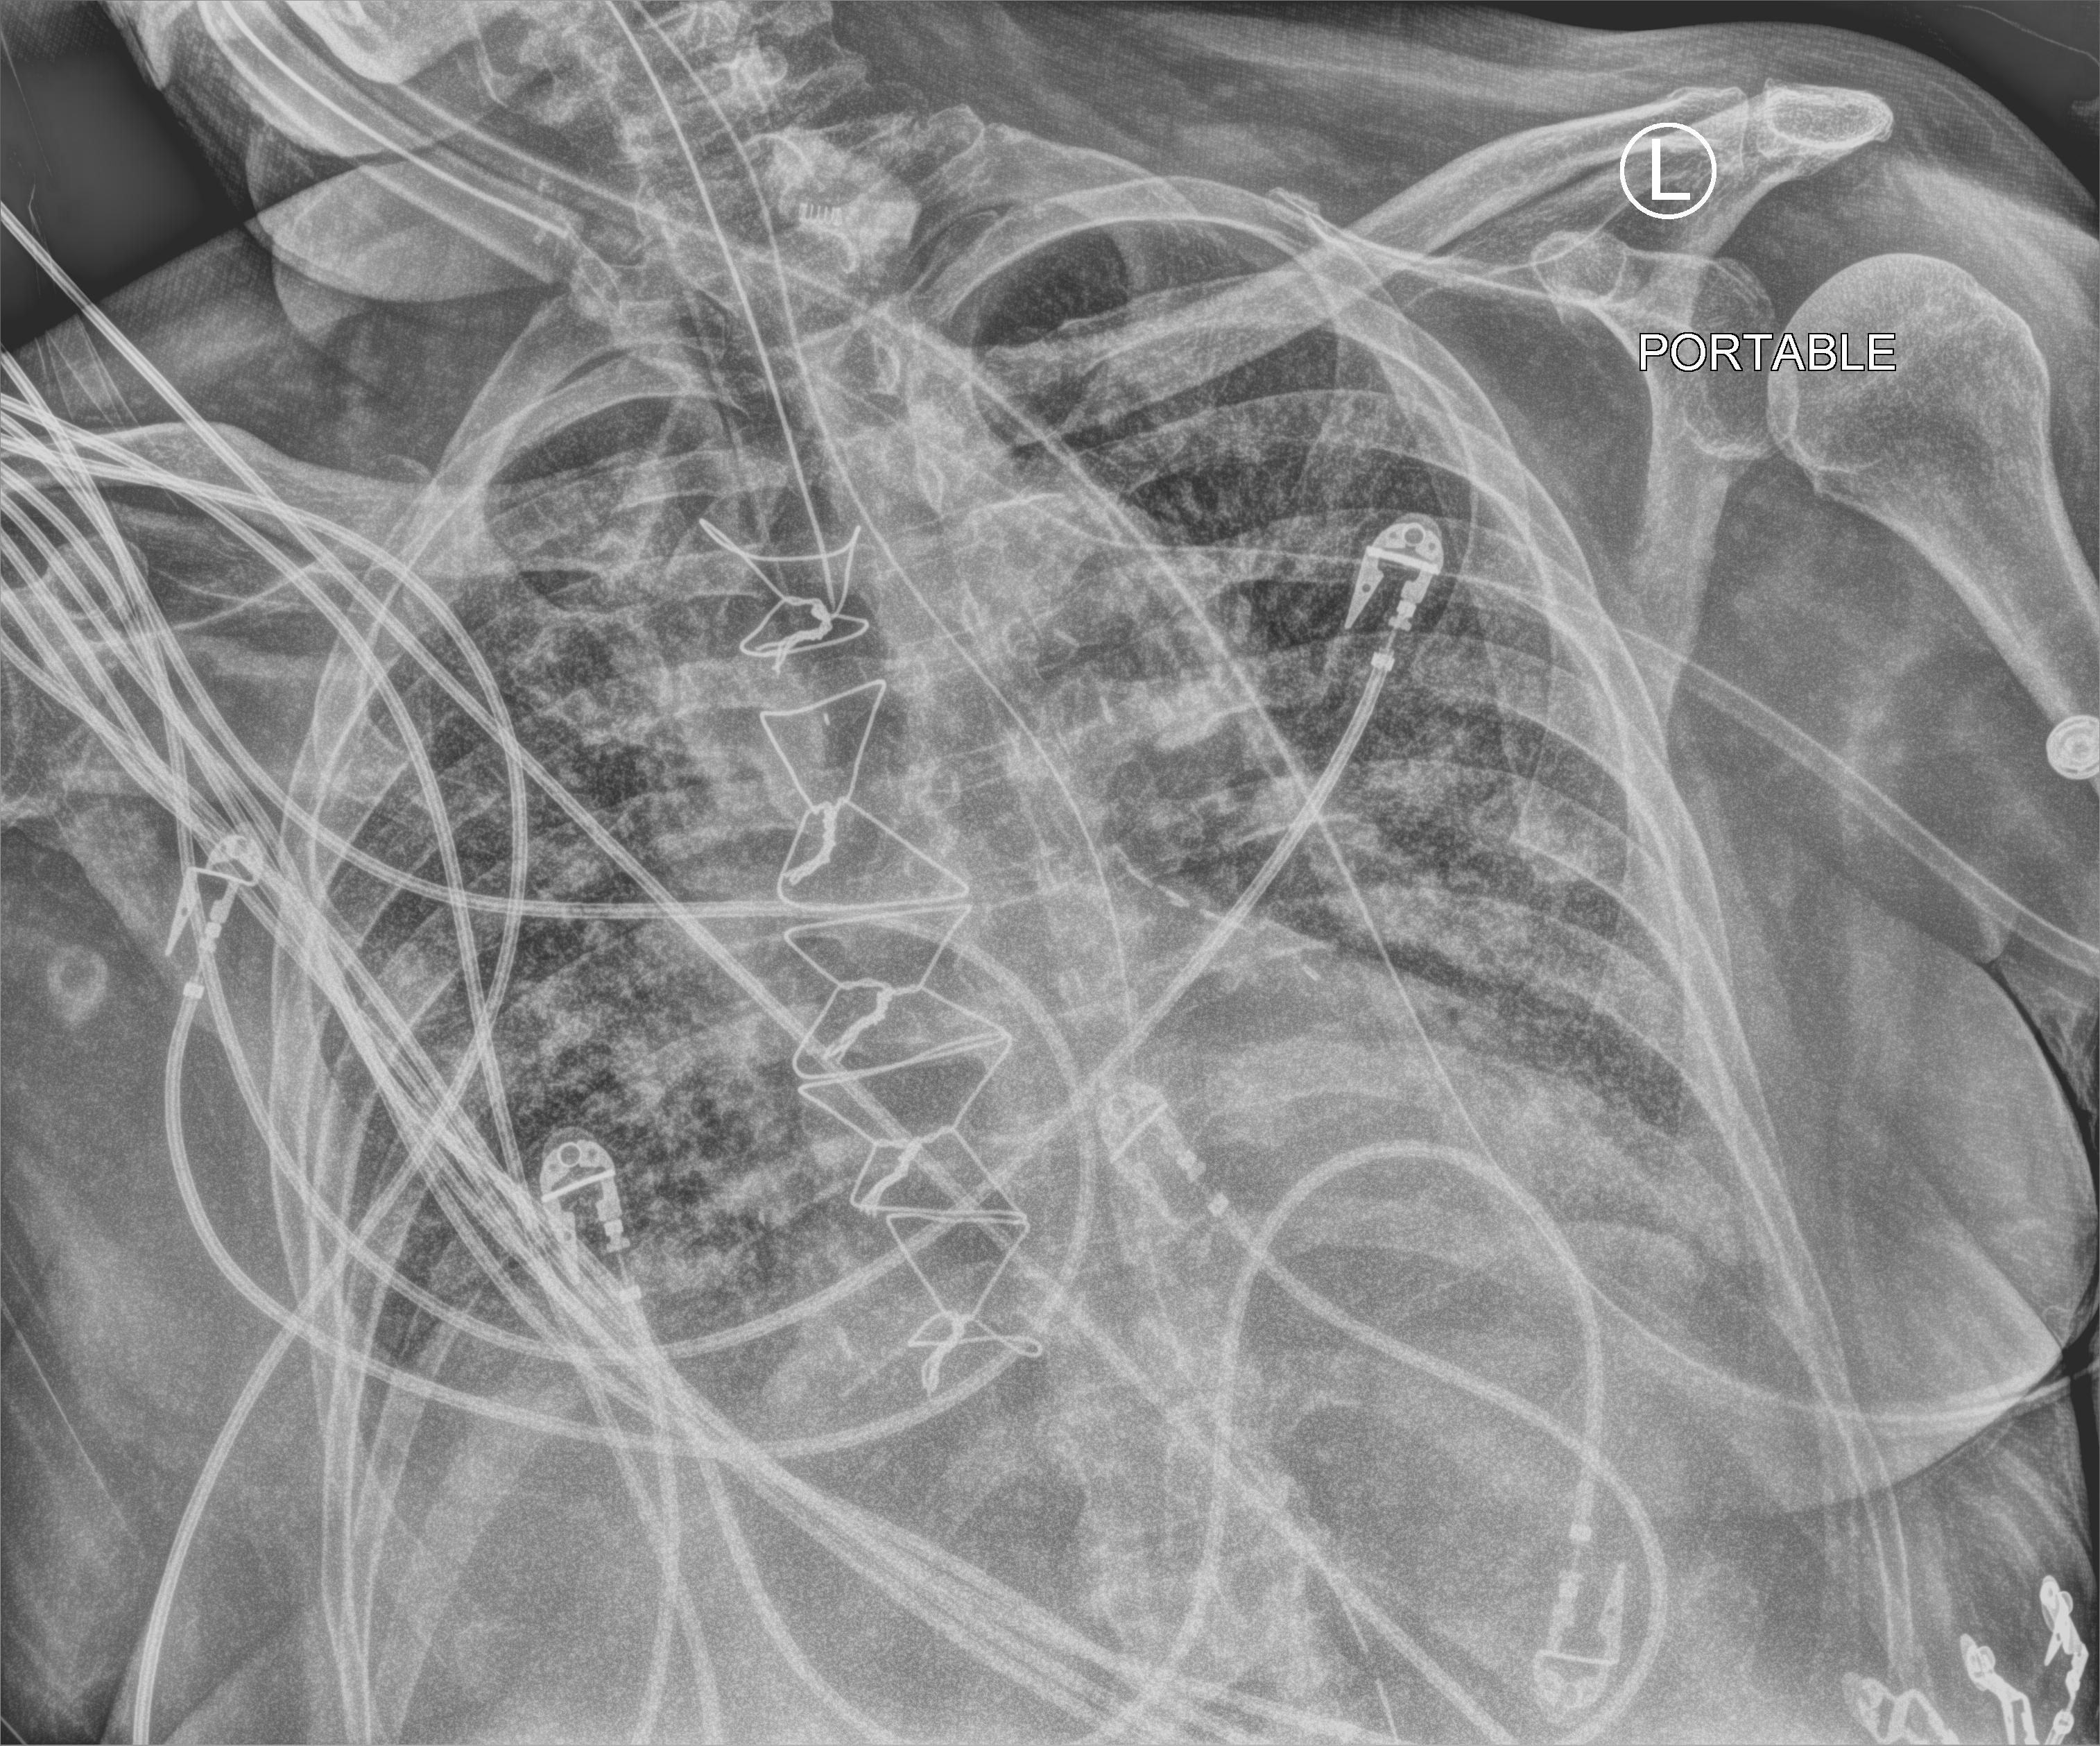
Portable chest radiograph, anteroposterior (AP) projection. Male patient hospitalised with COVID-19, age 75–90 years.
Admission-level facts for this patient (not findings on this image; timing relative to this image not recorded):
- diabetes (admission record): no
- mechanically ventilated during this hospital stay: yes
- admitted to intensive care during this hospital stay: yes